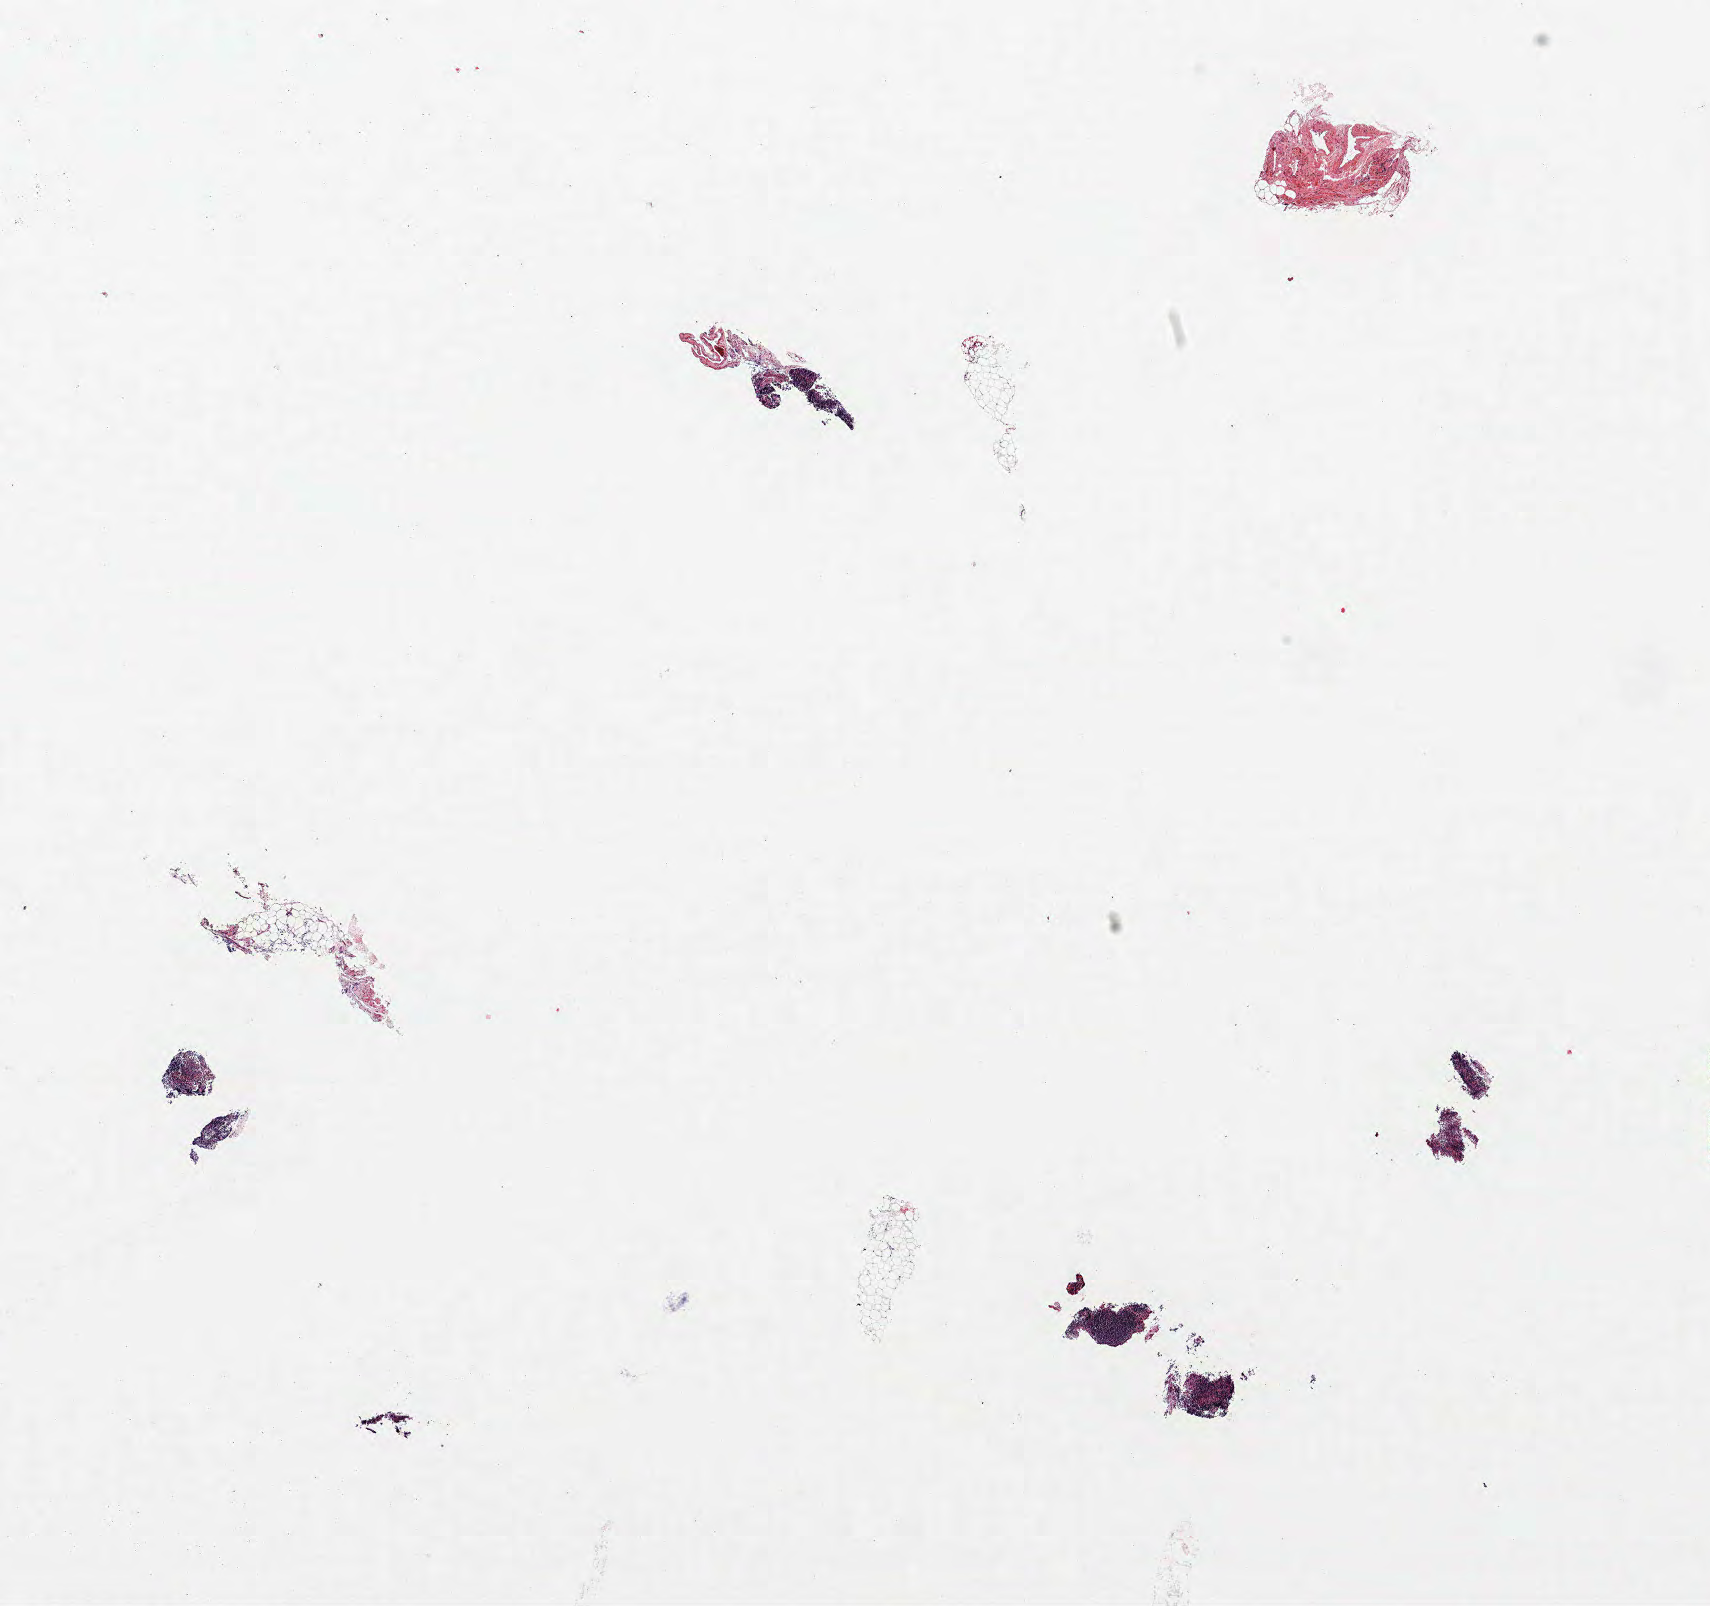
Whole-slide histology image, Hematoxylin and eosin (H&E) stained — a low-resolution overview of the entire scanned area, about 13.7 x 12.9 mm (acquisition: 40x scan), FFPE section, lung. Female, age 58 at enrolment. Former smoker at enrolment. Grade: poorly differentiated (G3).
Tumour size (pathology): 37 mm. Participant's lung-cancer diagnosis: Acinar cell carcinoma (ICD-O-3 8550/3). Stage (AJCC 6th edition): IIIA. Primary tumour location (clinical record): left upper lobe.